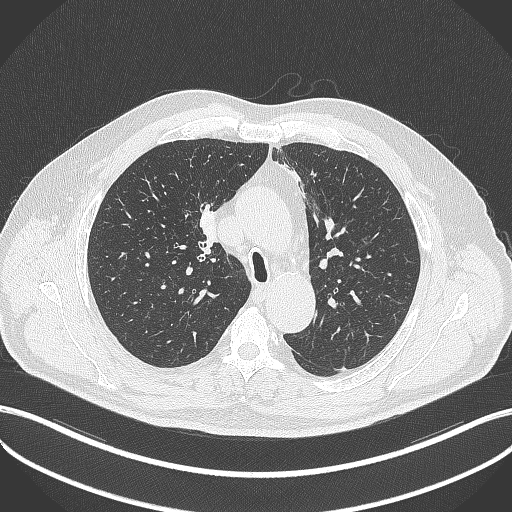
Chest CT, one axial slice. Slice 268 of 411 in the series (ordered by position). Reconstruction kernel B70f. 120 kVp. Lung window (W 1500 / L -600 HU). 512 × 512 image matrix. Male patient, age 60 years. From the clinical record (not read from this slice): clinical TNM (as recorded): T1b N1 M0.
Annotated regions visible in this slice (rectangle marked by the reading radiologist):
- lung tumour (recorded histology: squamous cell carcinoma): bounding box [x1, y1, x2, y2] px = [195, 203, 224, 248]